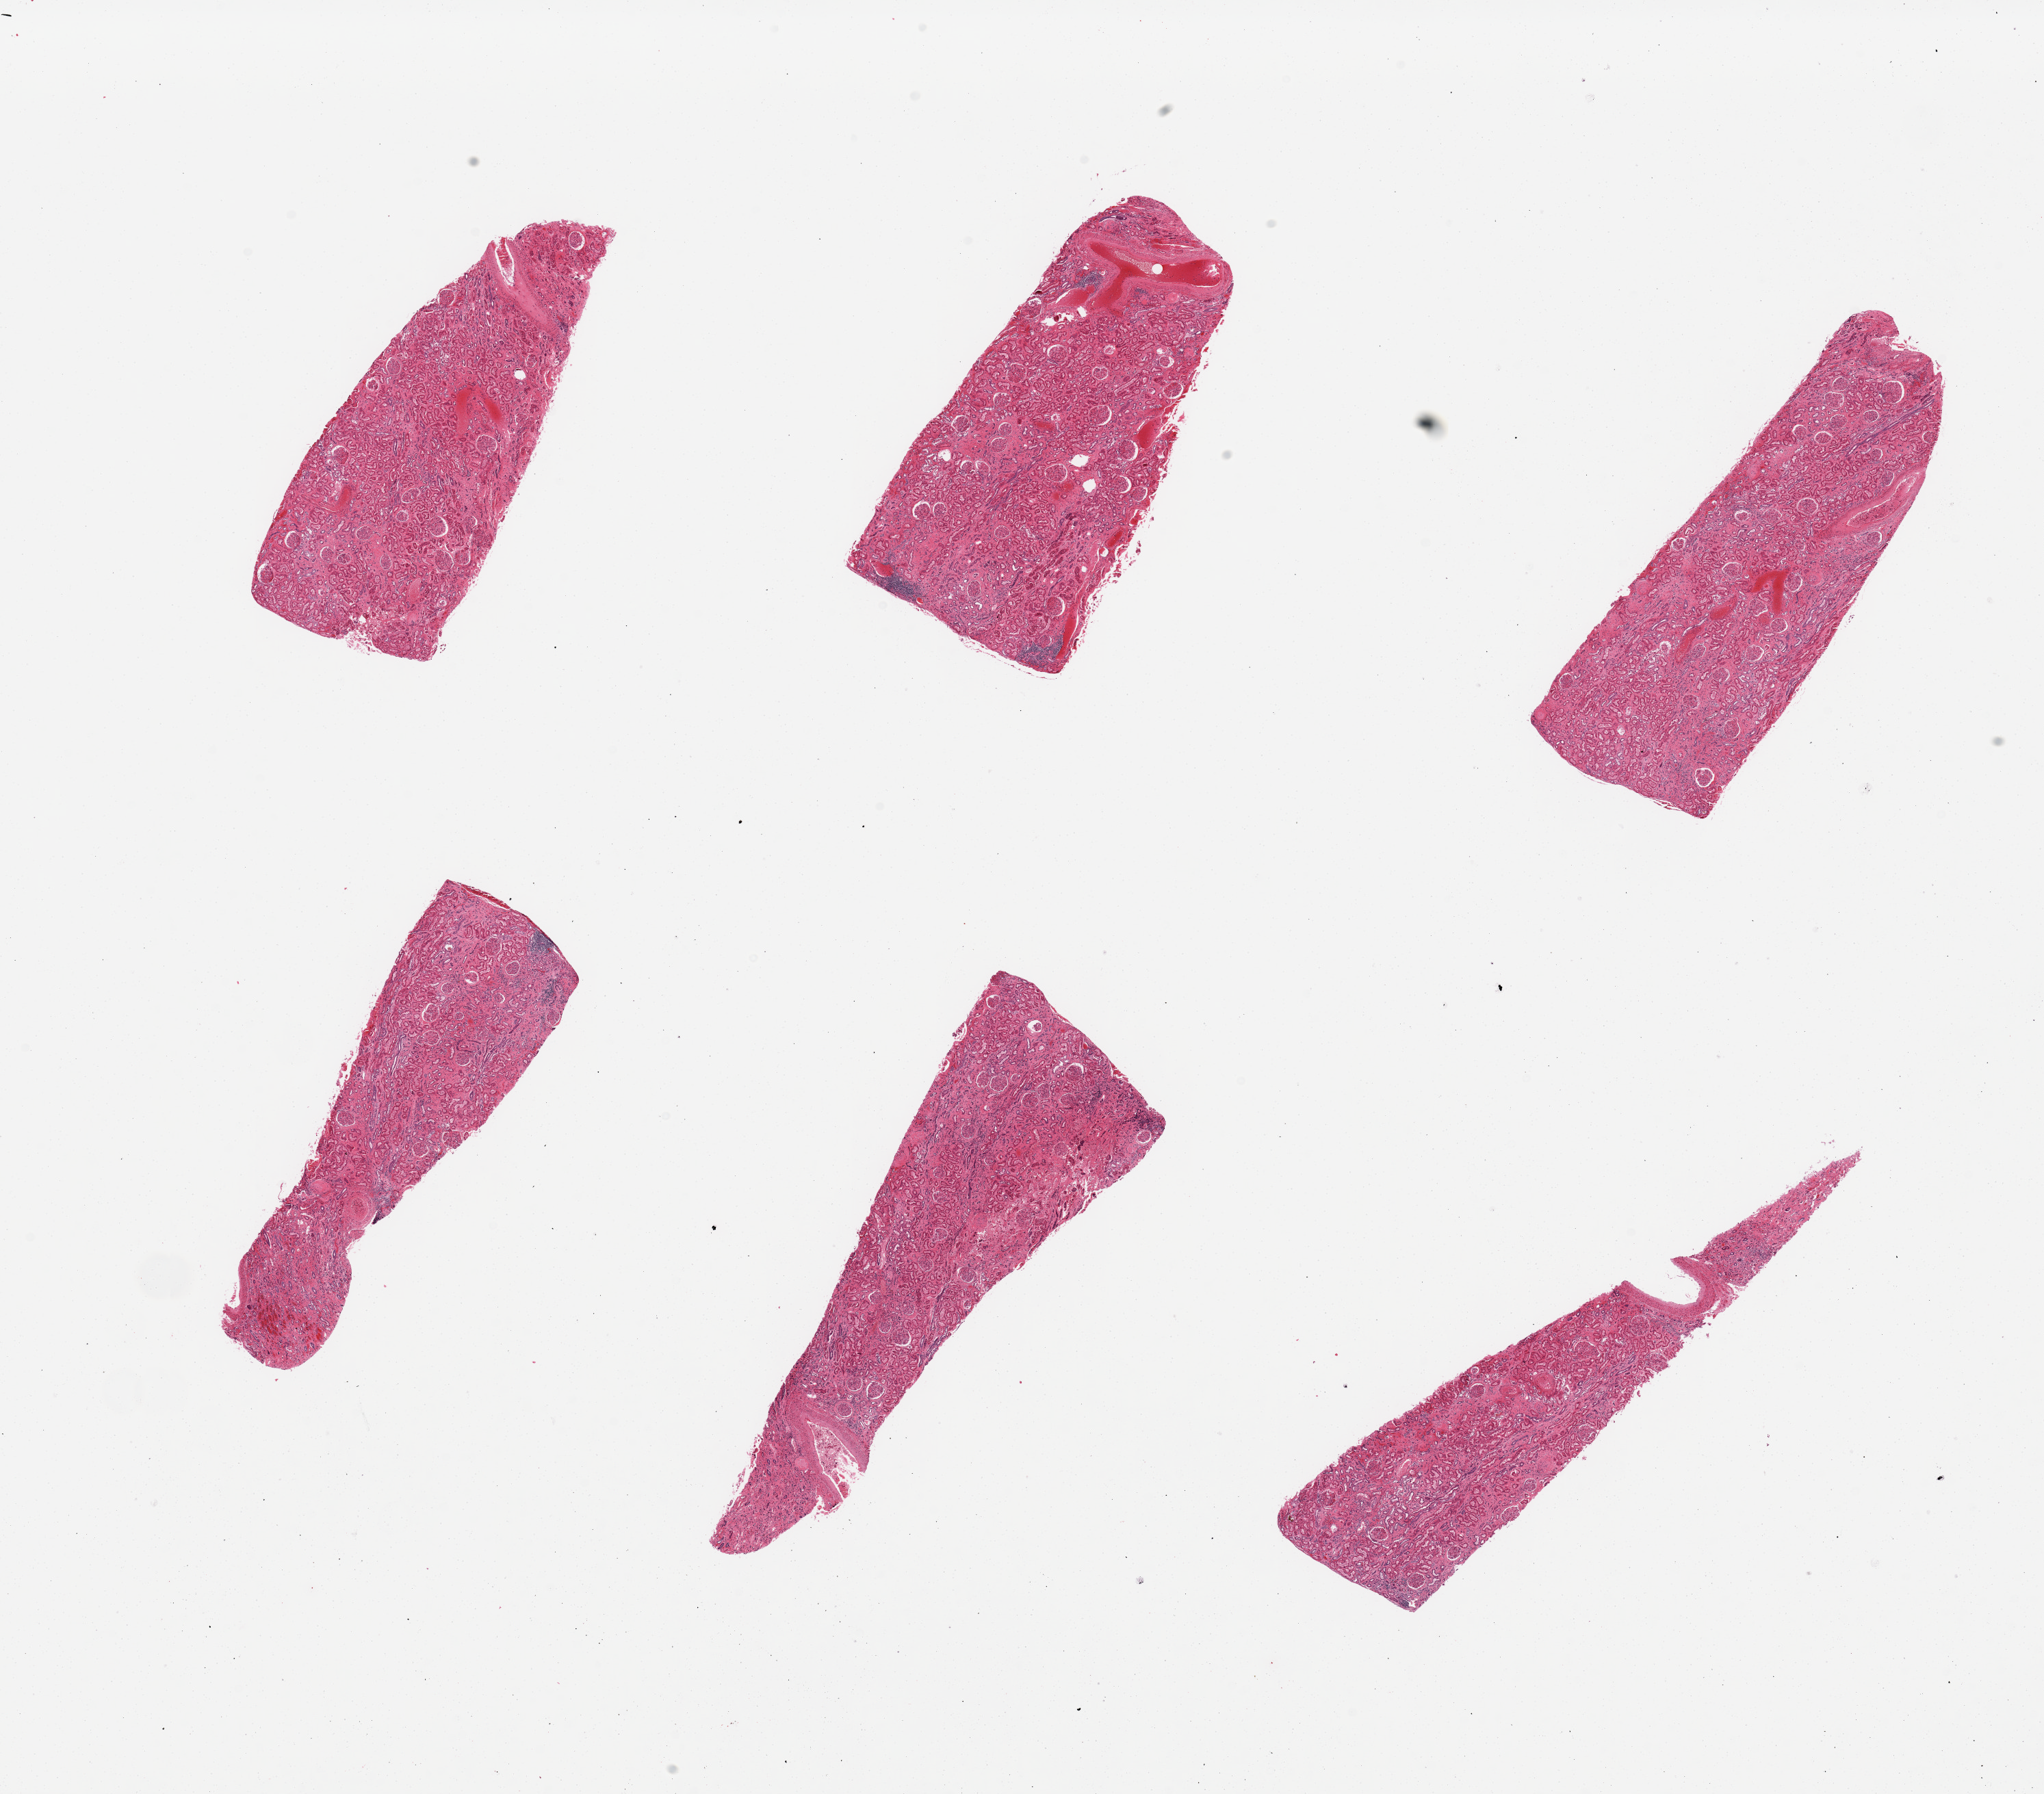
Hematoxylin and eosin (H&E) whole-slide image, shown as a low-resolution overview of the whole scanned area (about 23.6 x 20.7 mm, from a 20x scan); PAXgene-fixed, paraffin-embedded tissue; target tissue: renal cortex; tissue donor sample. Female donor.
Pathologist's review note for this sample: 6 pieces; occasional sclerosed glomerulus.